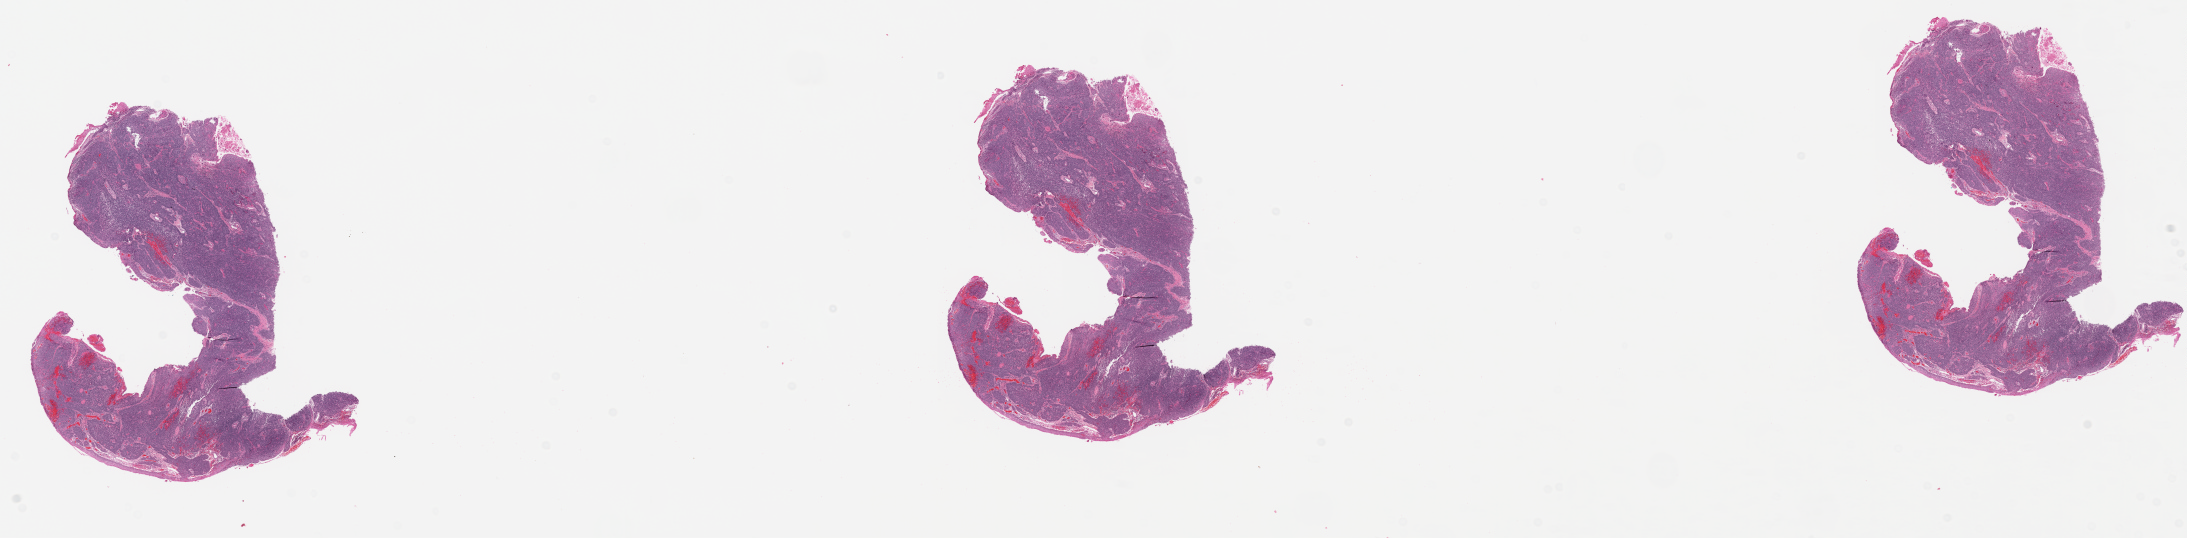
Whole-slide histology image, H&E, low-resolution overview of the scanned area, about 34.6 x 8.5 mm. FFPE section. Primary tumour sample from the head and neck. Male, age 51 years at initial diagnosis. Histologic grade: G2 (moderately differentiated).
Pathologic diagnosis: Squamous cell carcinoma, NOS. Laterality: left.